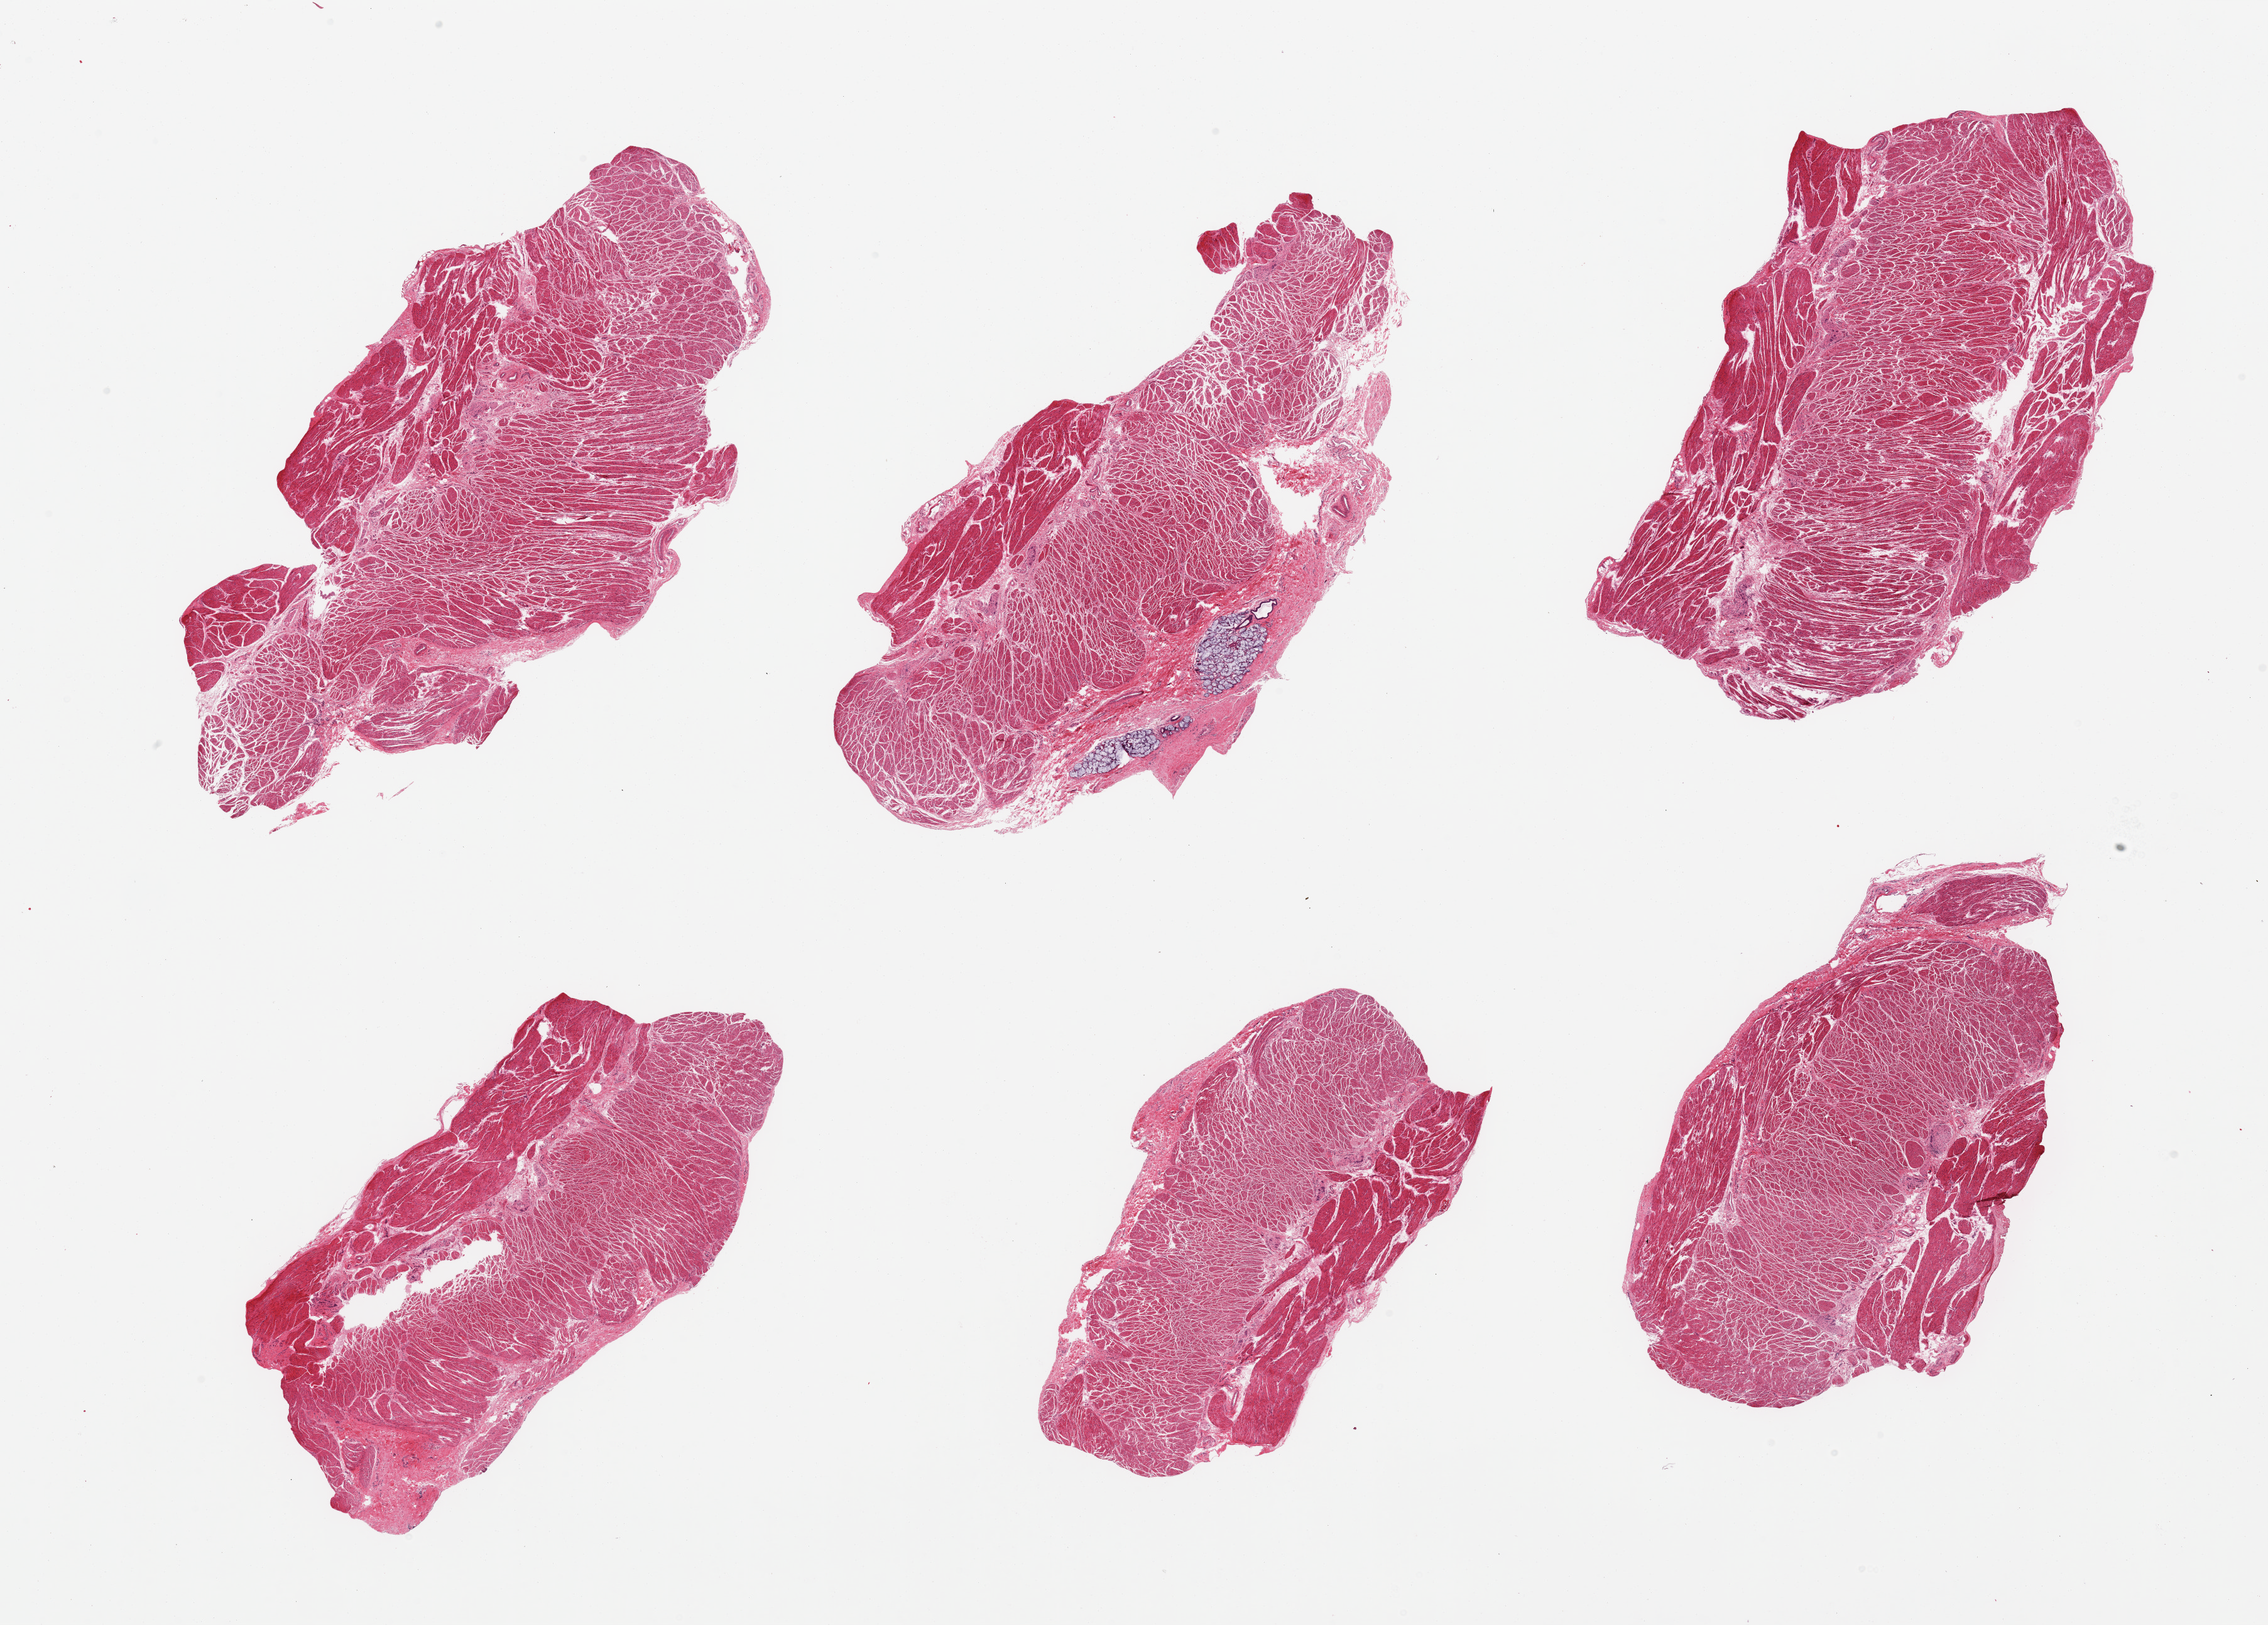
Whole-slide image, hematoxylin and eosin (H&E) stain, whole scanned area (about 28.5 x 20.5 mm) shown as a low-resolution overview. PAXgene-fixed paraffin-embedded (PFPE) section. Section of esophageal muscle (target tissue). Tissue donor sample. Male donor.
Reviewer comment on this tissue sample: 6 pieces; well trimmed except for submucosal glands in 1 piece (5%).